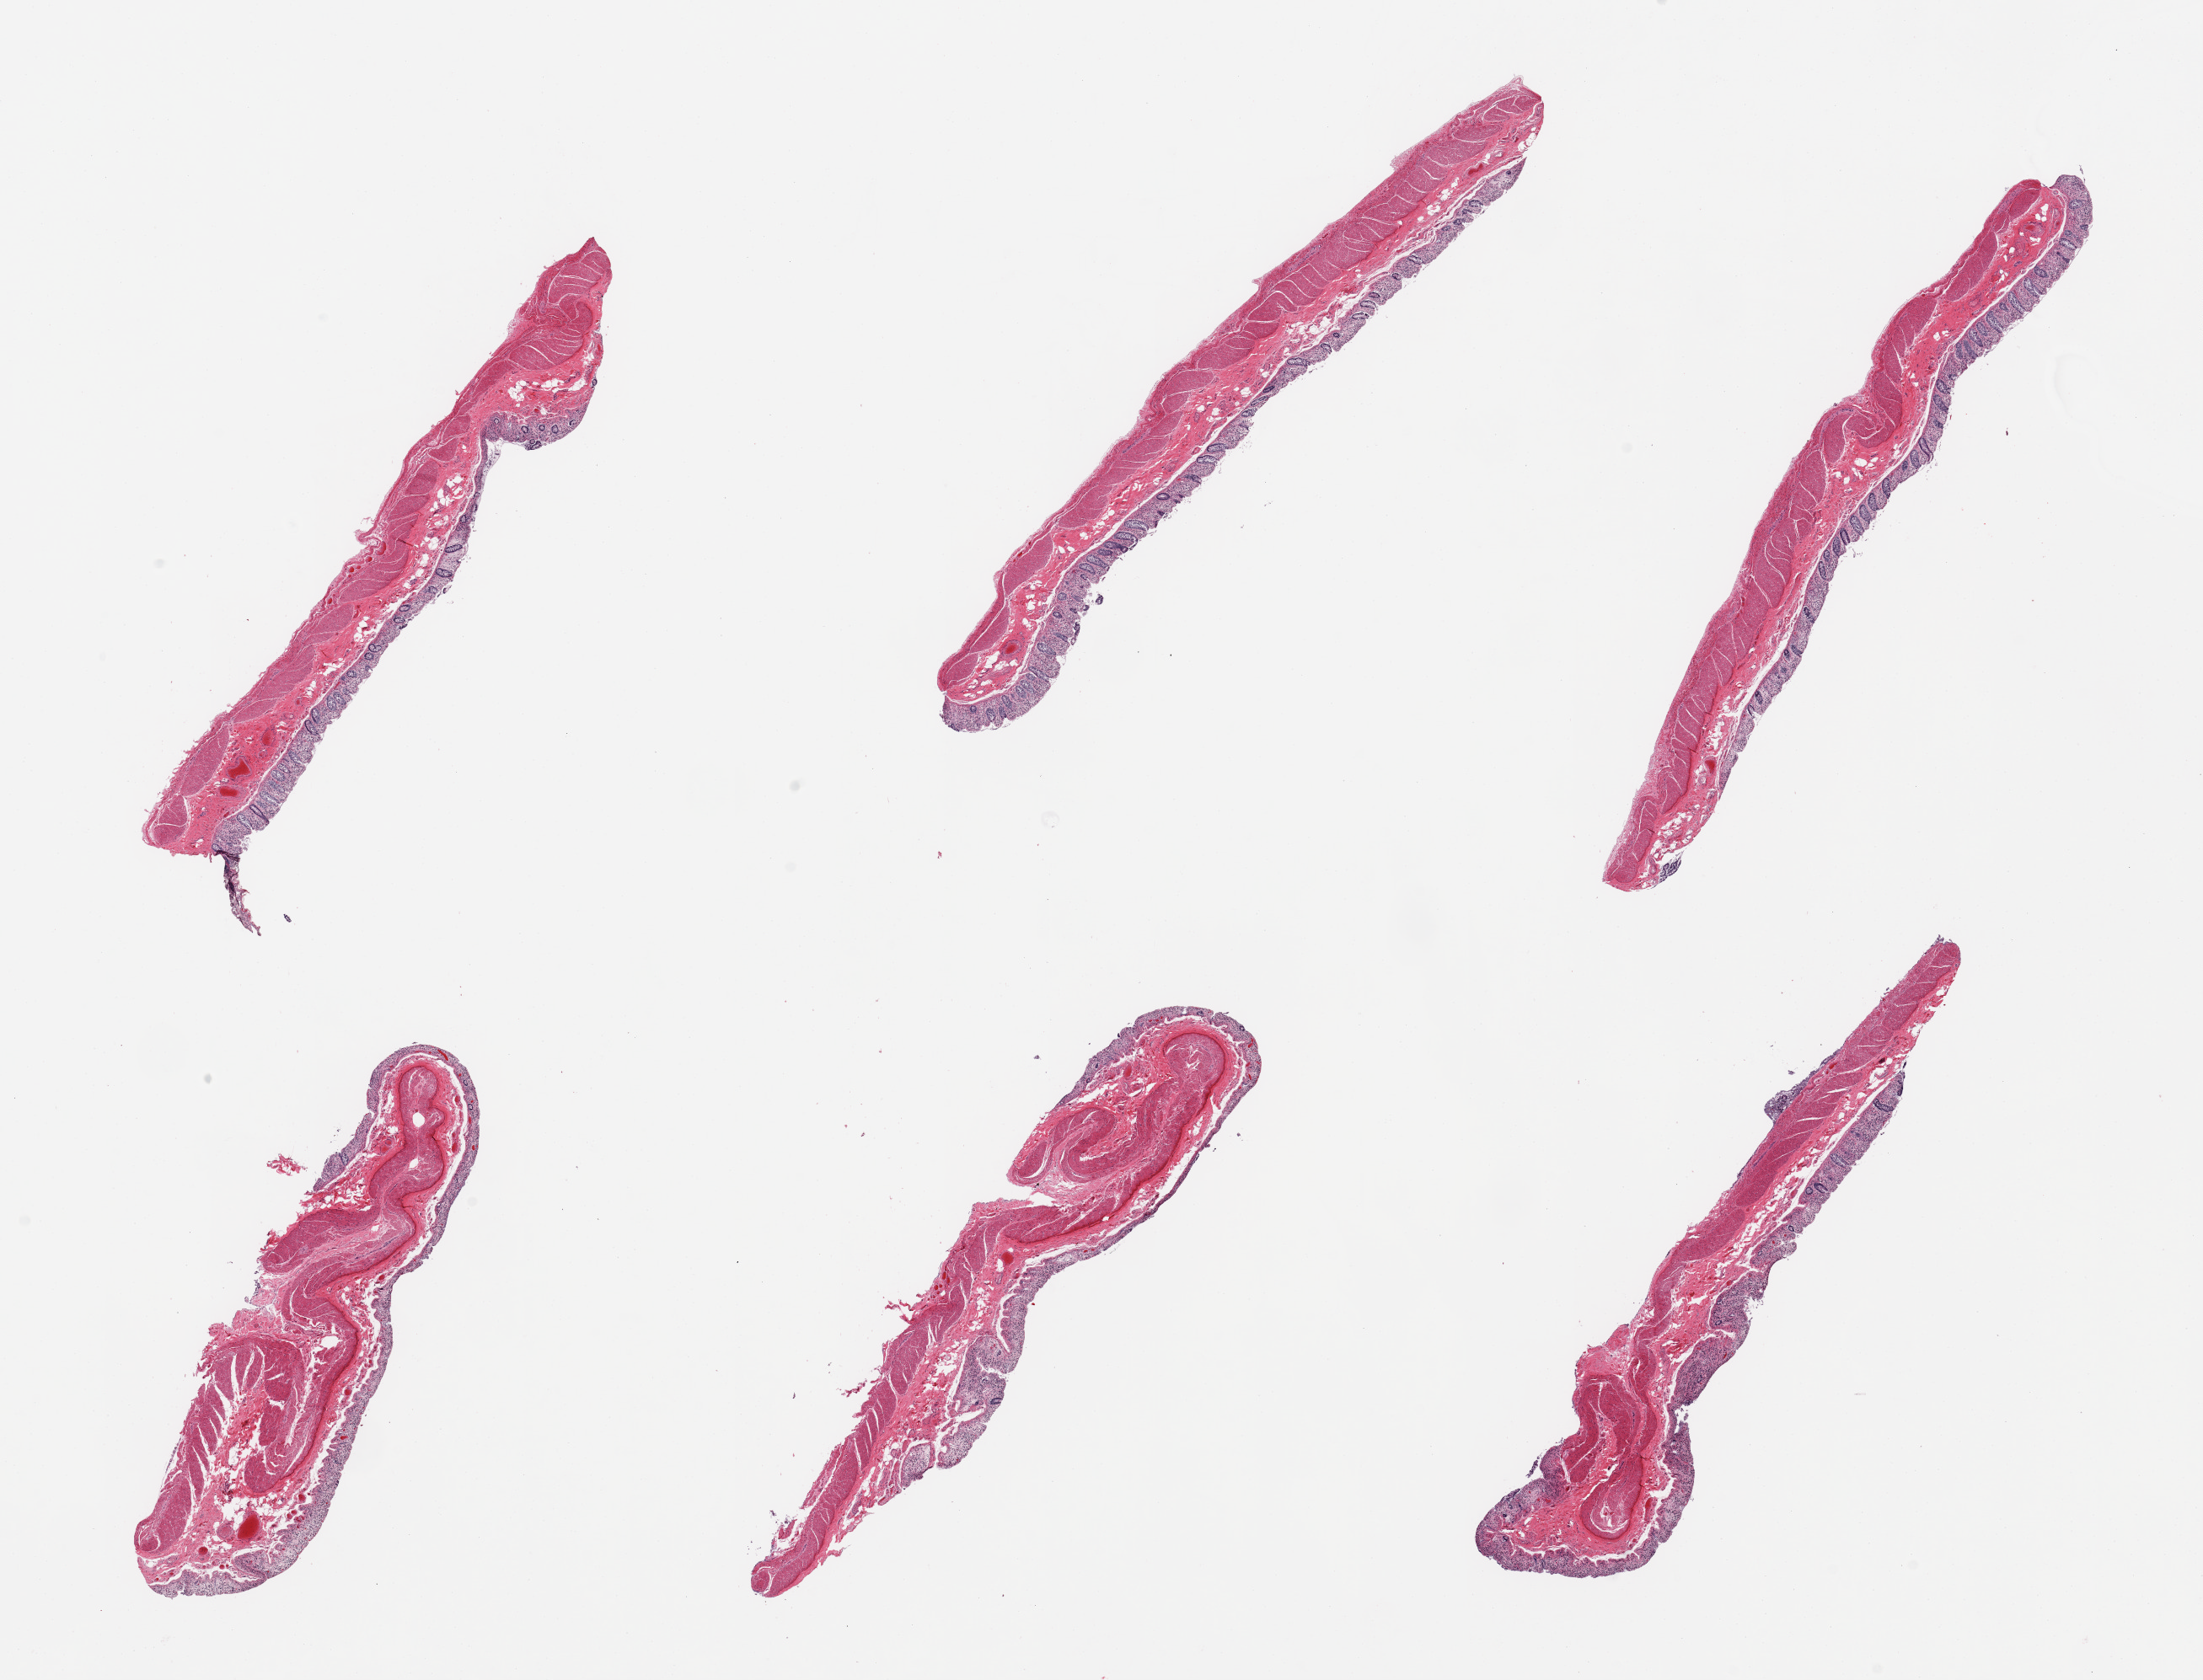
Whole-slide image, haematoxylin and eosin stain — whole scanned area (about 20.7 x 15.8 mm) shown as a low-resolution overview, PAXgene-fixed paraffin-embedded (PFPE) section, sampled site (target tissue): transverse colon, tissue donor sample. Donor sex: female.
Reviewer comment on this tissue sample: 6 pieces; mucosa largely autolyzed; muscularis intact (1).